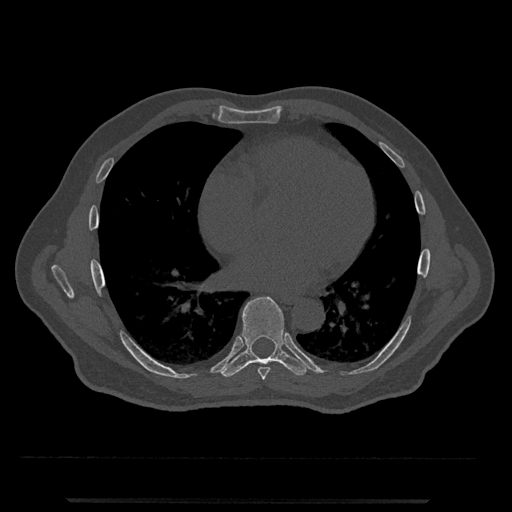
CT including the spine, one axial slice. Slice 646 of 797 in the series (ordered by position). Bone window (W 1800 / L 400 HU). 0.5 mm slice thickness. 512 × 512 image matrix, field of view 419 × 419 mm. Male patient, age 63 years. Case-level facts recorded for this patient, not image findings: primary cancer: prostate.
Annotated regions visible in this slice (semi-automatically segmented with operator editing):
- T7 vertebra: bounding box <258,367,270,380> (left, top, right, bottom; pixels)
- T8 vertebra: <222,296,313,377>